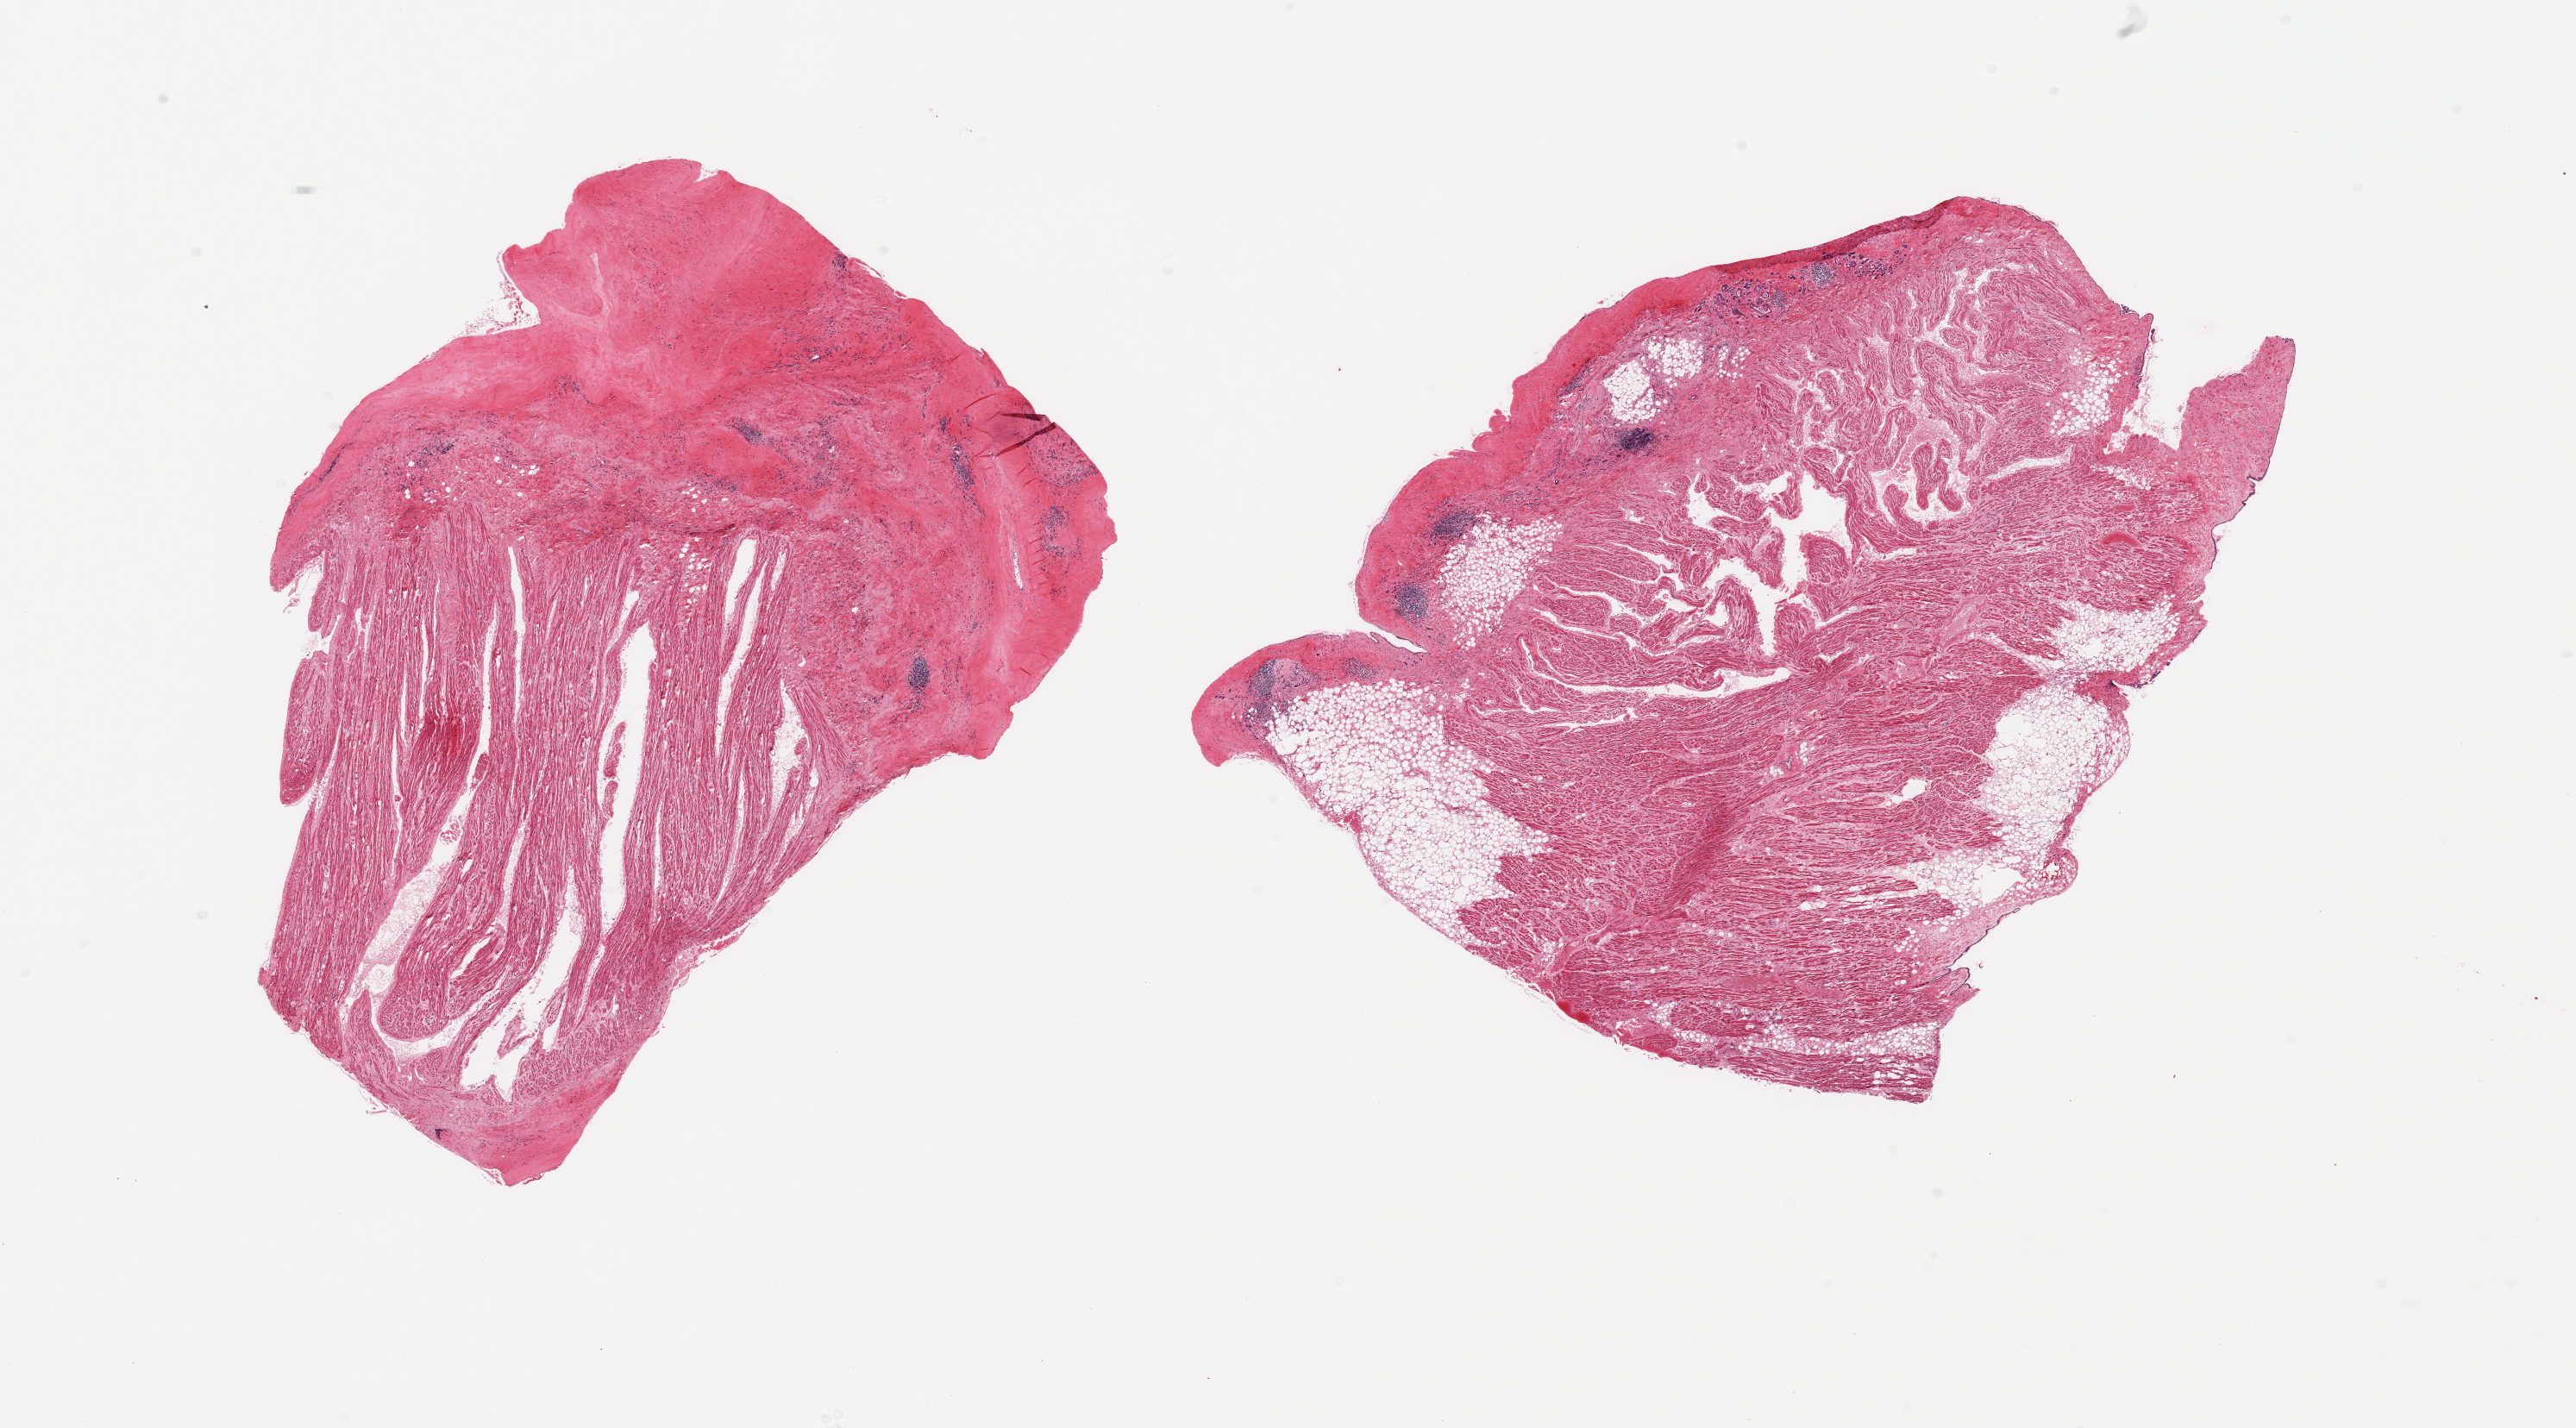
Digitized hematoxylin and eosin (H&E)-stained section — whole scanned area (about 23.6 x 13.1 mm, slide scanned at 20x) shown as a low-resolution overview; PAXgene-fixed paraffin-embedded (PFPE) section; target tissue: auricular appendage; donor tissue sample. Donor sex: female.
Reviewer comment on this tissue sample: 2 pieces: 1 has 40% external fibrous content, other has 30% fibroadipose content; both have several small lymphoid collections in the outer fibrous areas.